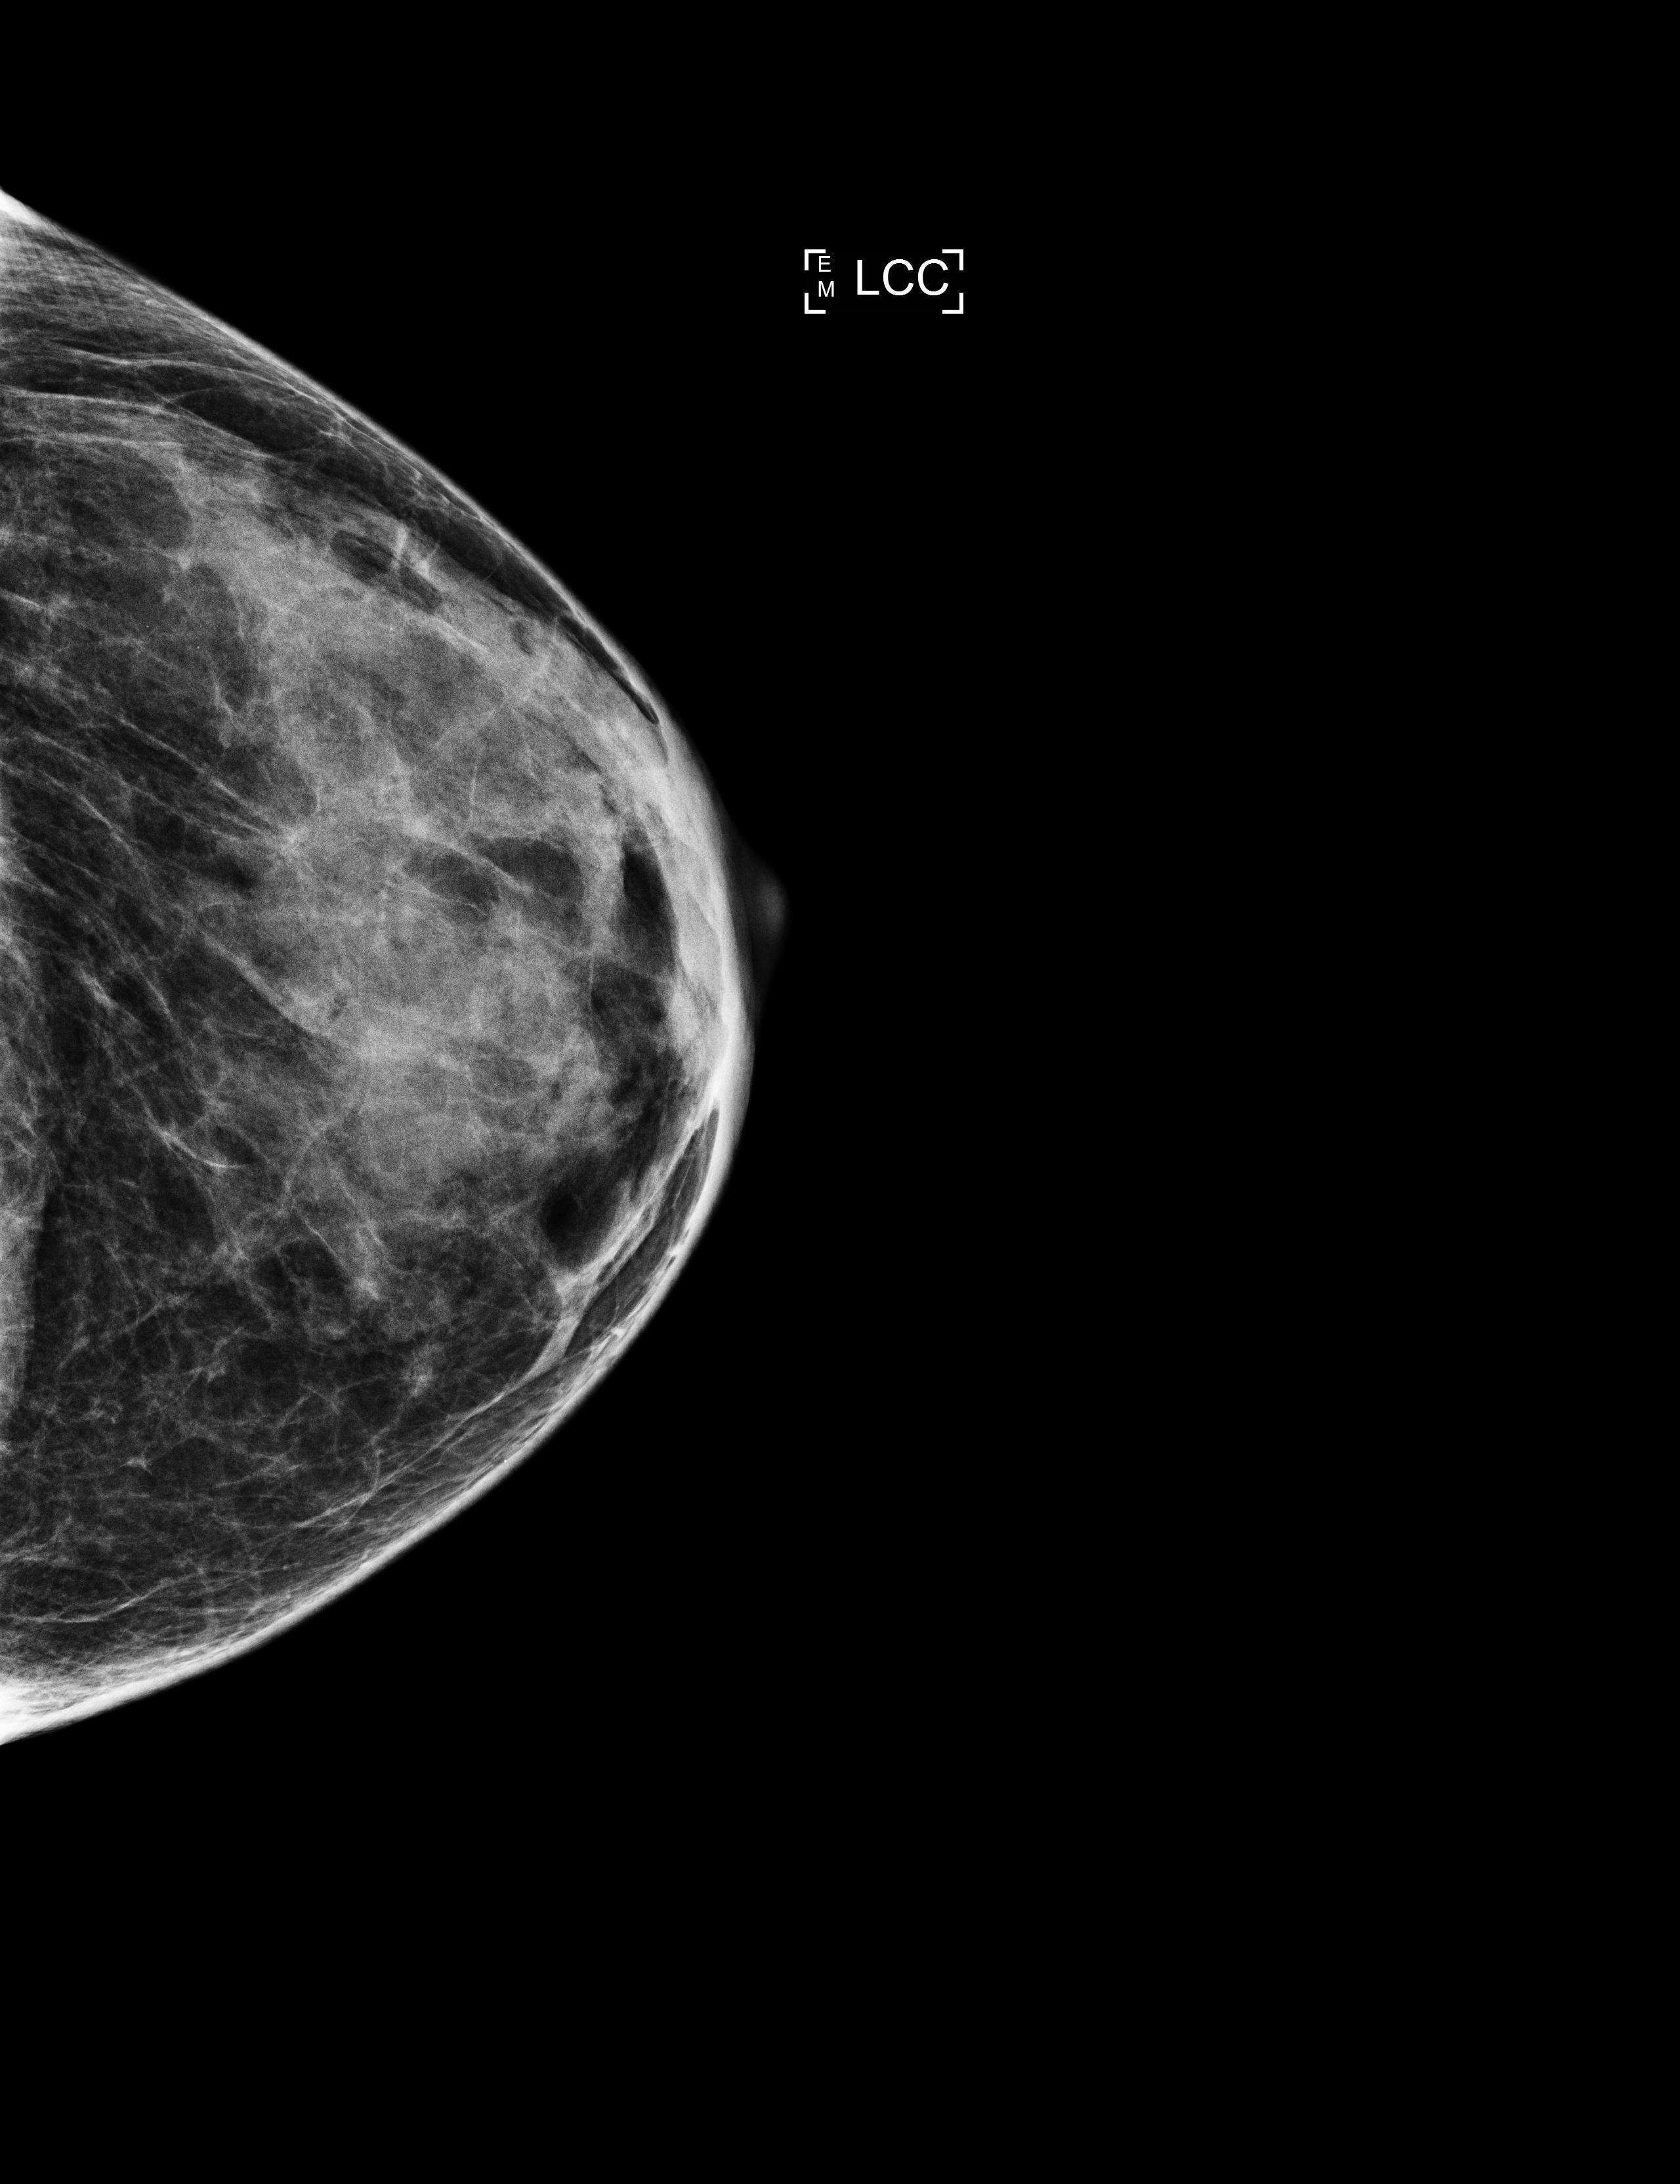
Screening examination, system: Selenia Dimensions. Female patient, age 66 years.
Image type: full-field digital mammogram. Breast: left. Projection: CC view.